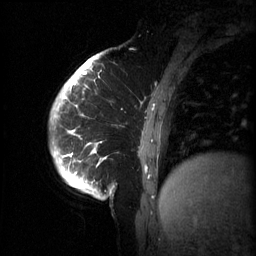
Breast MRI (dynamic contrast-enhanced), one sagittal slice. Position 10 of 60 along the scan axis. 3 images stored at this slice position (order not interpretable as contrast timing). 1.5 T. TE 4.2 ms, TR 11 ms. 2 mm slice thickness. 256 × 256 image matrix, field of view 220 × 220 mm. Female patient, age 51 years.
Outlined on this slice (semi-automatically segmented with operator editing):
- analysis volume of interest (the breast-tissue region the enhancement analysis was run in; not a lesion): bounding box (x1, y1, x2, y2) in pixels: (63, 80, 185, 201)
- tumour enhancement mask (voxels above the 70 % enhancement threshold inside the analysis volume of interest): (64, 82, 153, 173)